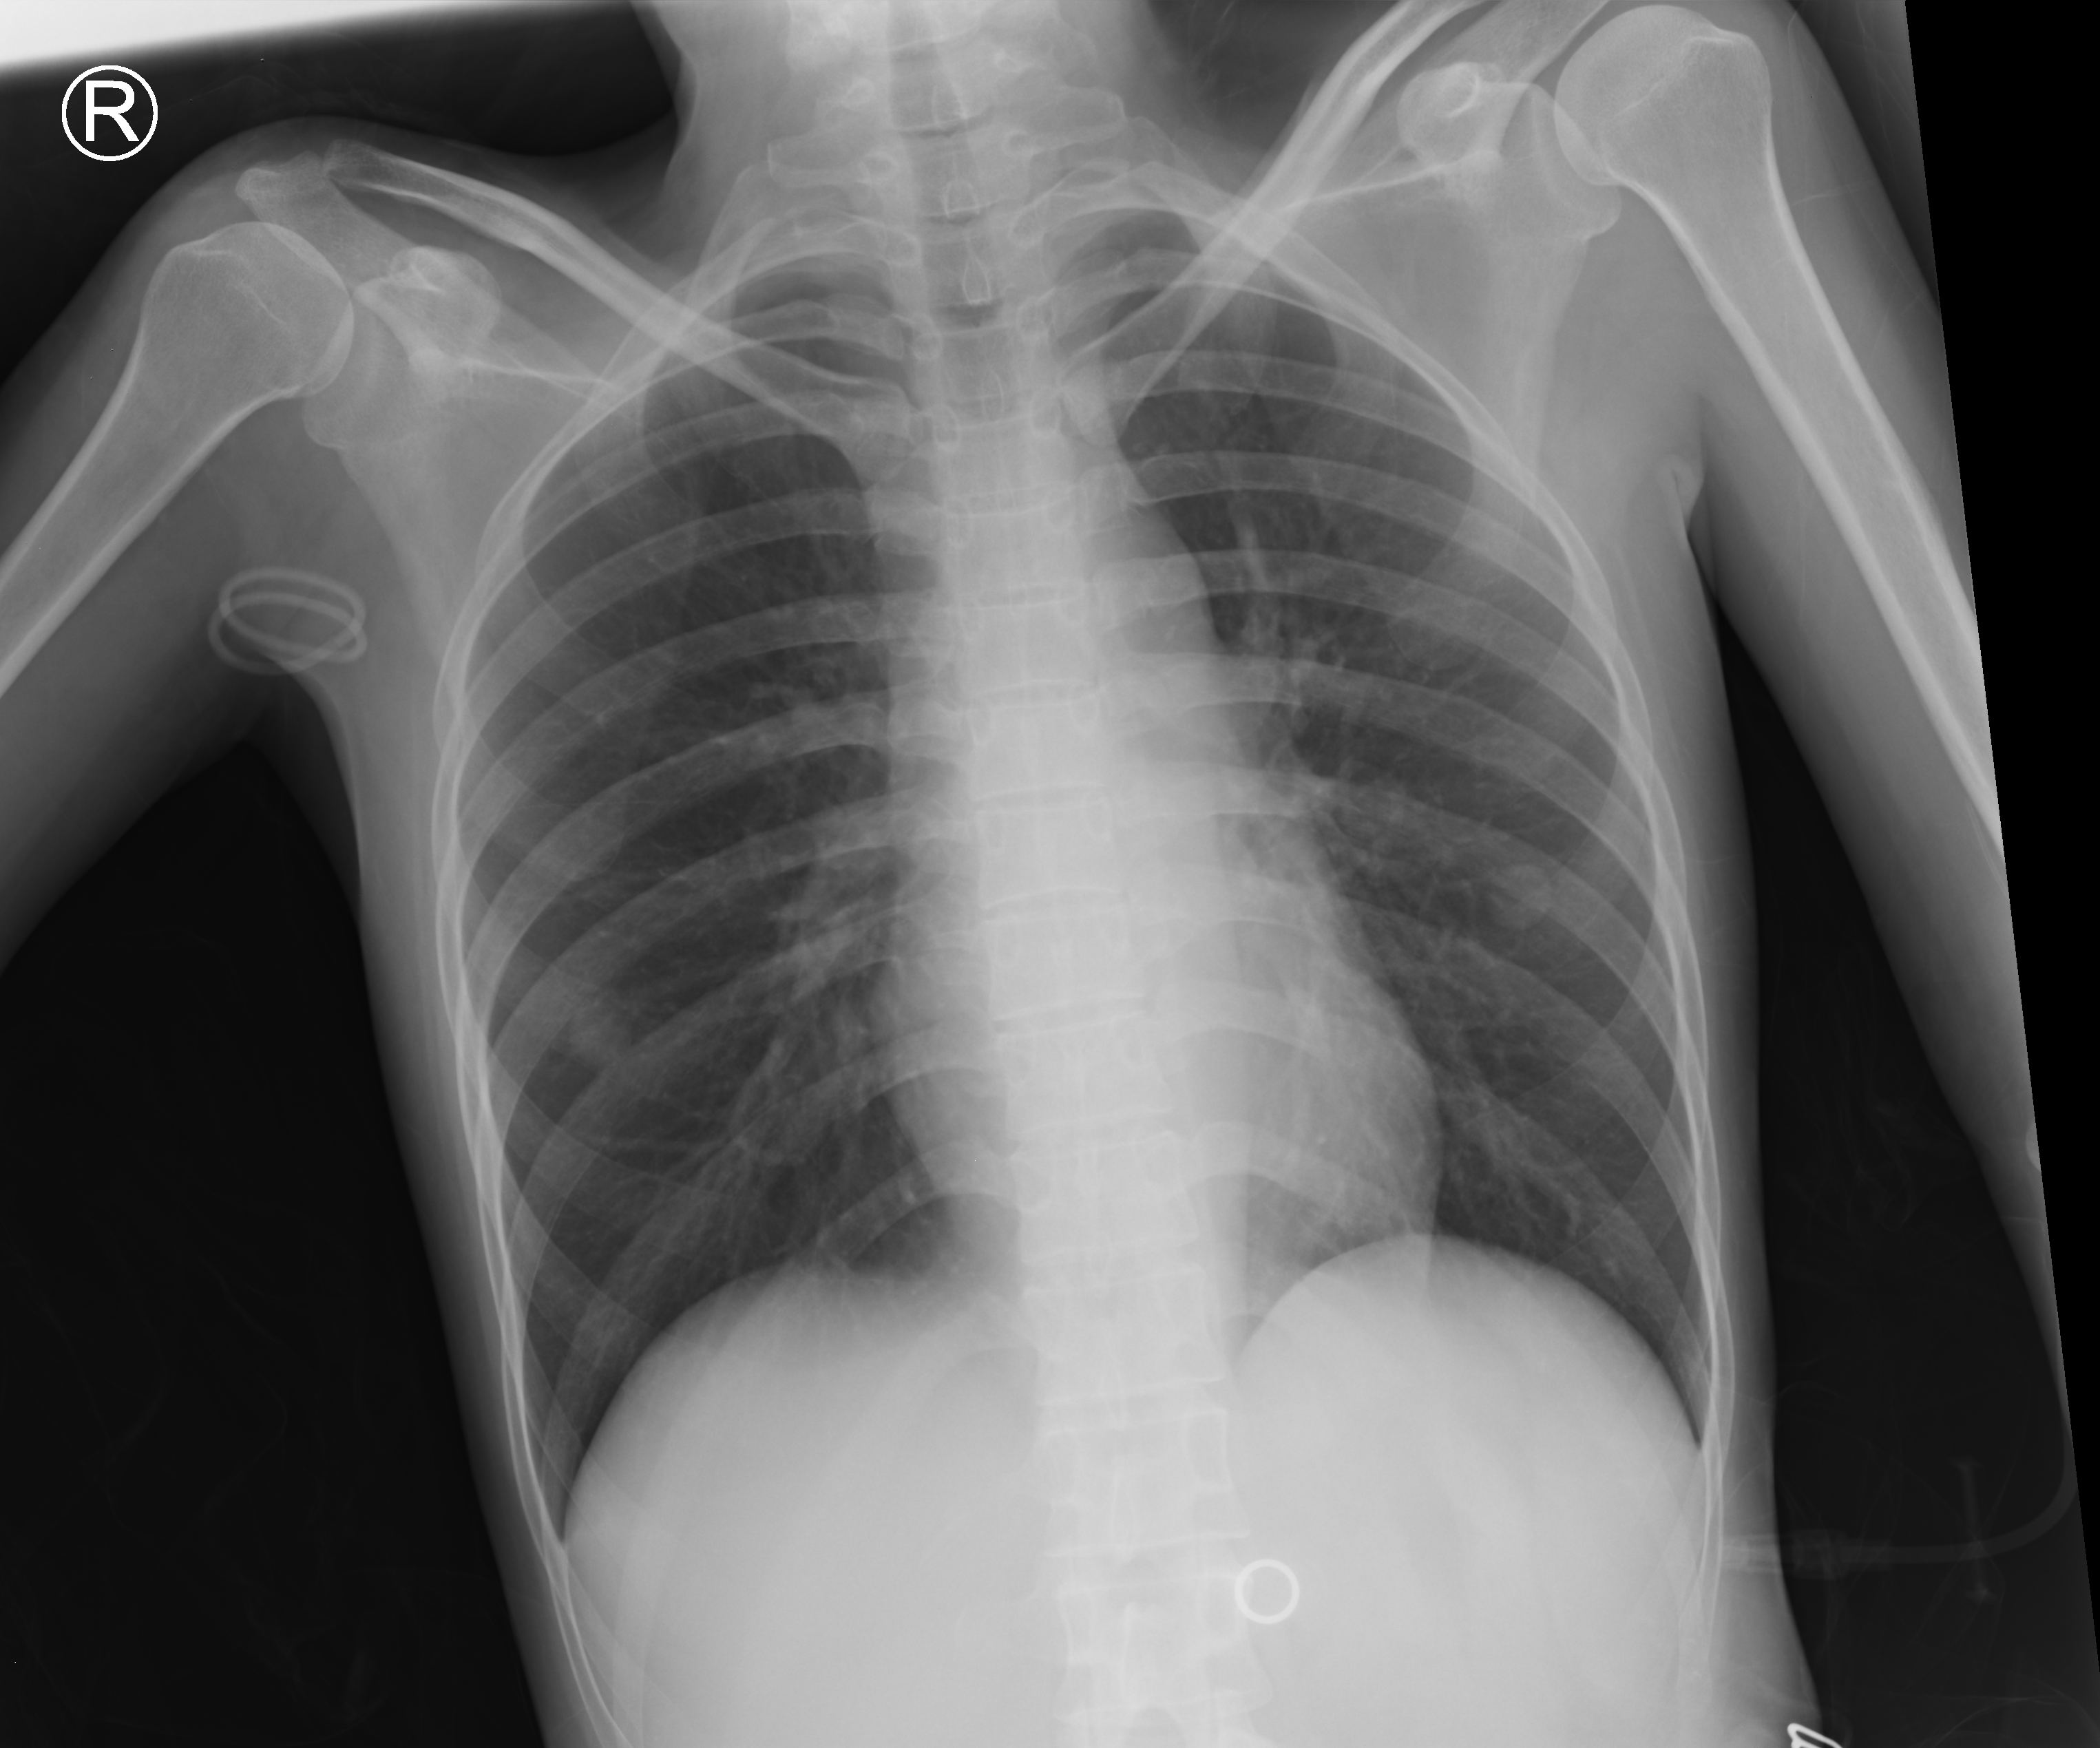
Portable chest radiograph, anteroposterior (AP) projection. Patient hospitalised with COVID-19; female, aged 18–59 years.
Admission-level facts for this patient (not findings on this image; timing relative to this image not recorded):
- admitted to intensive care during this hospital stay: no
- mechanically ventilated during this hospital stay: no
- smoking status (admission record): never